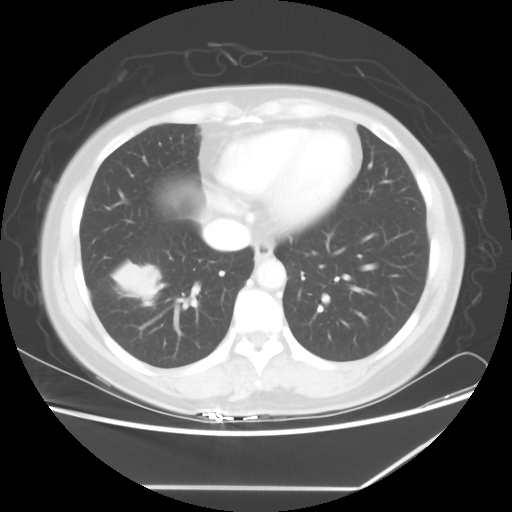
Chest CT, one axial slice; slice 21 of 60 in the series (ordered by position); reconstruction kernel STANDARD; 100 kVp; lung window (W 1500 / L -600 HU); 5 mm slice thickness; 512 × 512 image matrix, field of view 374 × 374 mm. Female patient, age 42 years. Case-level facts recorded for this patient, not image findings: clinical TNM (as recorded): T2 N1 M0.
Annotated regions visible in this slice (bounding box drawn by a radiologist):
- lung tumour (recorded histology: adenocarcinoma): bounding box [x1, y1, x2, y2] px = [116, 257, 160, 308]